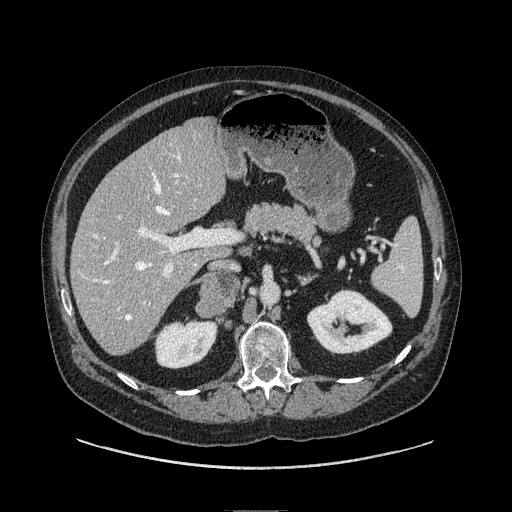
Contrast-enhanced abdominal CT, one axial slice. Slice 46 of 149 in the series (ordered by position). Soft-tissue window (W 400 / L 40 HU). 1.25 mm slice thickness. 512 × 512 image matrix, field of view 440 × 440 mm. Male patient. From the clinical record (not read from this slice): diagnosis: adrenocortical carcinoma; tumour side: right adrenal; tumour size at pathology: 7.5 cm; Ki-67 index: 15 %; stage (as recorded): 2.
Structures marked on this image (semi-automatically segmented with operator editing):
- mass: bounding box (x1, y1, x2, y2) in pixels: (196, 274, 238, 314)